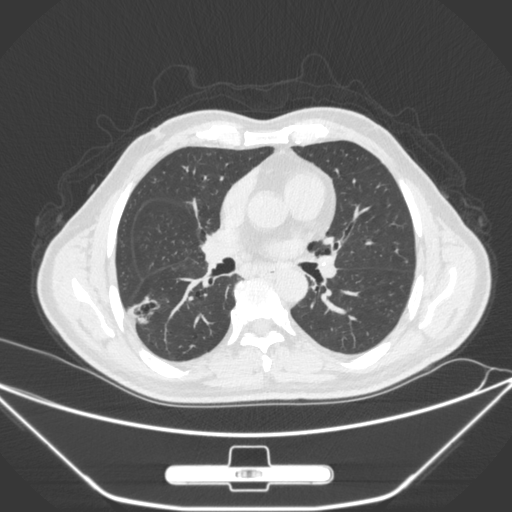
Chest CT, one axial slice. Position 152 of 310 along the scan axis. 120 kVp. Lung window (W 1500 / L -600 HU). 1 mm slice thickness. 512 × 512 image matrix. Patient: male, 71 years. Case-level facts recorded for this patient, not image findings: clinical TNM (as recorded): T1c N0 M0; histopathological grade: G2.
Structures marked on this image (rectangle marked by the reading radiologist):
- lung tumour (recorded histology: adenocarcinoma): box from (x=129, y=295) to (x=165, y=332) px